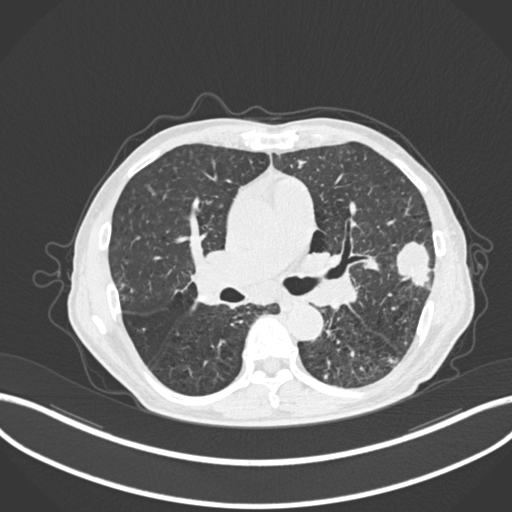
Chest CT, one axial slice. Position 136 of 287 along the scan axis. Reconstruction kernel B30f. Lung window (W 1500 / L -600 HU). 1 mm slice thickness. 512 × 512 image matrix. Male patient, age 74 years. Case-level facts recorded for this patient, not image findings: clinical TNM (as recorded): T2a N1 M0.
Annotated regions visible in this slice (rectangle marked by the reading radiologist):
- lung tumour (recorded histology: adenocarcinoma): bounding box [x1, y1, x2, y2] px = [393, 236, 433, 290]